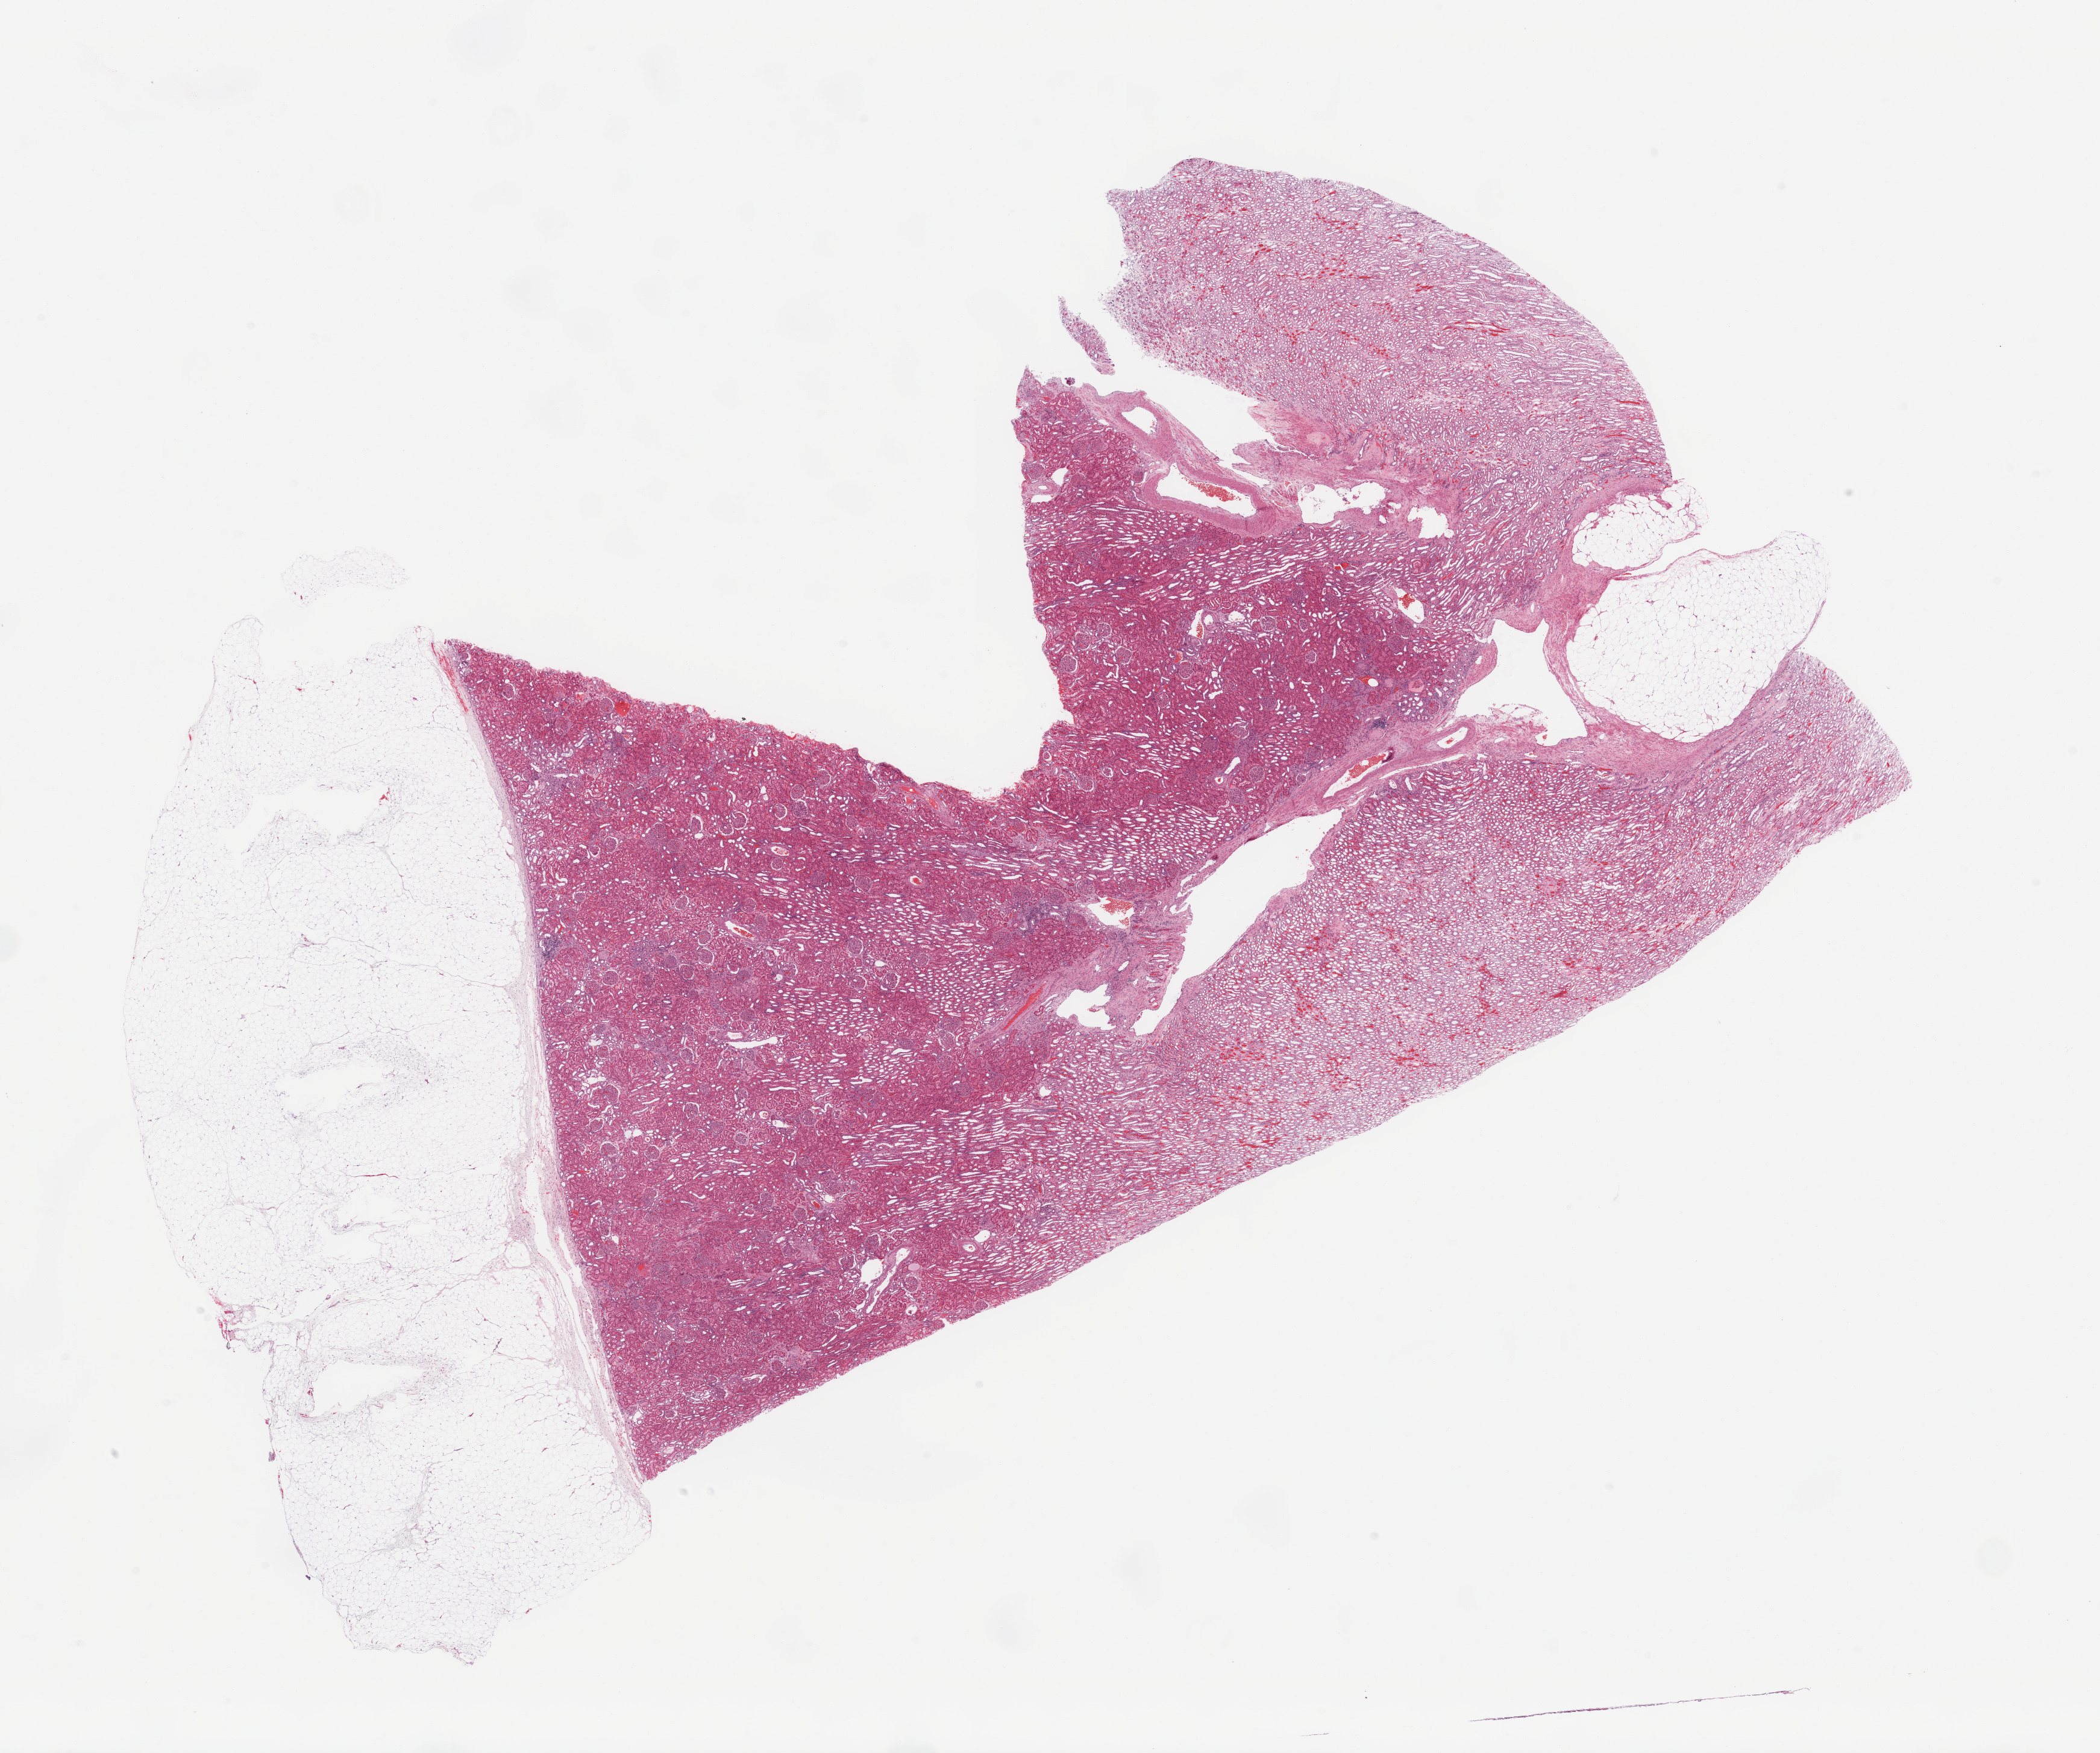
H&E-stained whole-slide image — a low-resolution overview of the entire scanned area, about 27.6 x 23.0 mm (slide scanned at 20x); normal (non-tumour) tissue sample, sampled site: kidney. Male, 55 y/o.
- this section: normal (non-tumour) tissue from the same patient
- patient diagnosis: Renal cell carcinoma, NOS